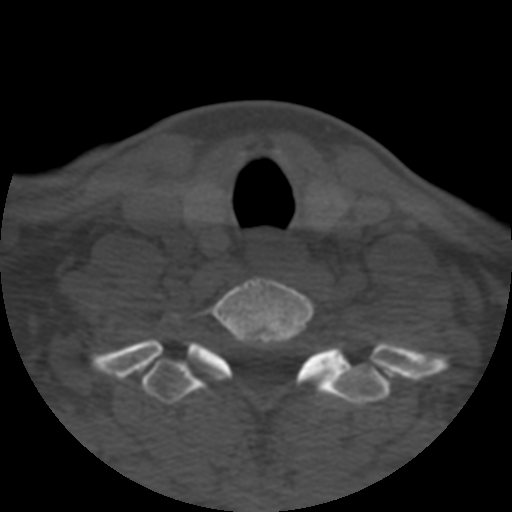
CT including the spine, one axial slice; position 456 of 508 along the scan axis; reconstruction kernel STANDARD; 120 kVp; bone window (W 1800 / L 400 HU); 512 × 512 image matrix, field of view 160 × 160 mm. Patient age 57 years. From the clinical record (not read from this slice): primary cancer: prostate.
Structures marked on this image (semi-automatically segmented with operator editing):
- T1 vertebra: bounding box <143,354,390,405> (left, top, right, bottom; pixels)